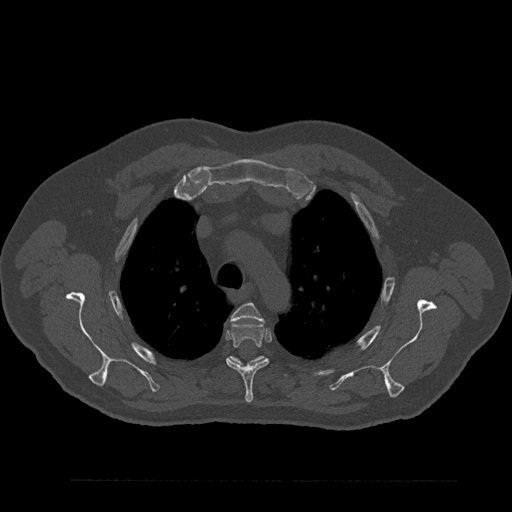
CT including the spine, one axial slice; slice 642 of 797 in the series (ordered by position); 120 kVp; bone window (W 1800 / L 400 HU); 512 × 512 image matrix. Male patient, age 61 years. Case-level facts recorded for this patient, not image findings: primary cancer: prostate.
Structures marked on this image (semi-automatic segmentation, software-assisted and operator-edited):
- T3 vertebra: bounding box <231,303,263,322> (left, top, right, bottom; pixels)
- T4 vertebra: <226,322,269,403>
- T5 vertebra: <229,356,288,377>